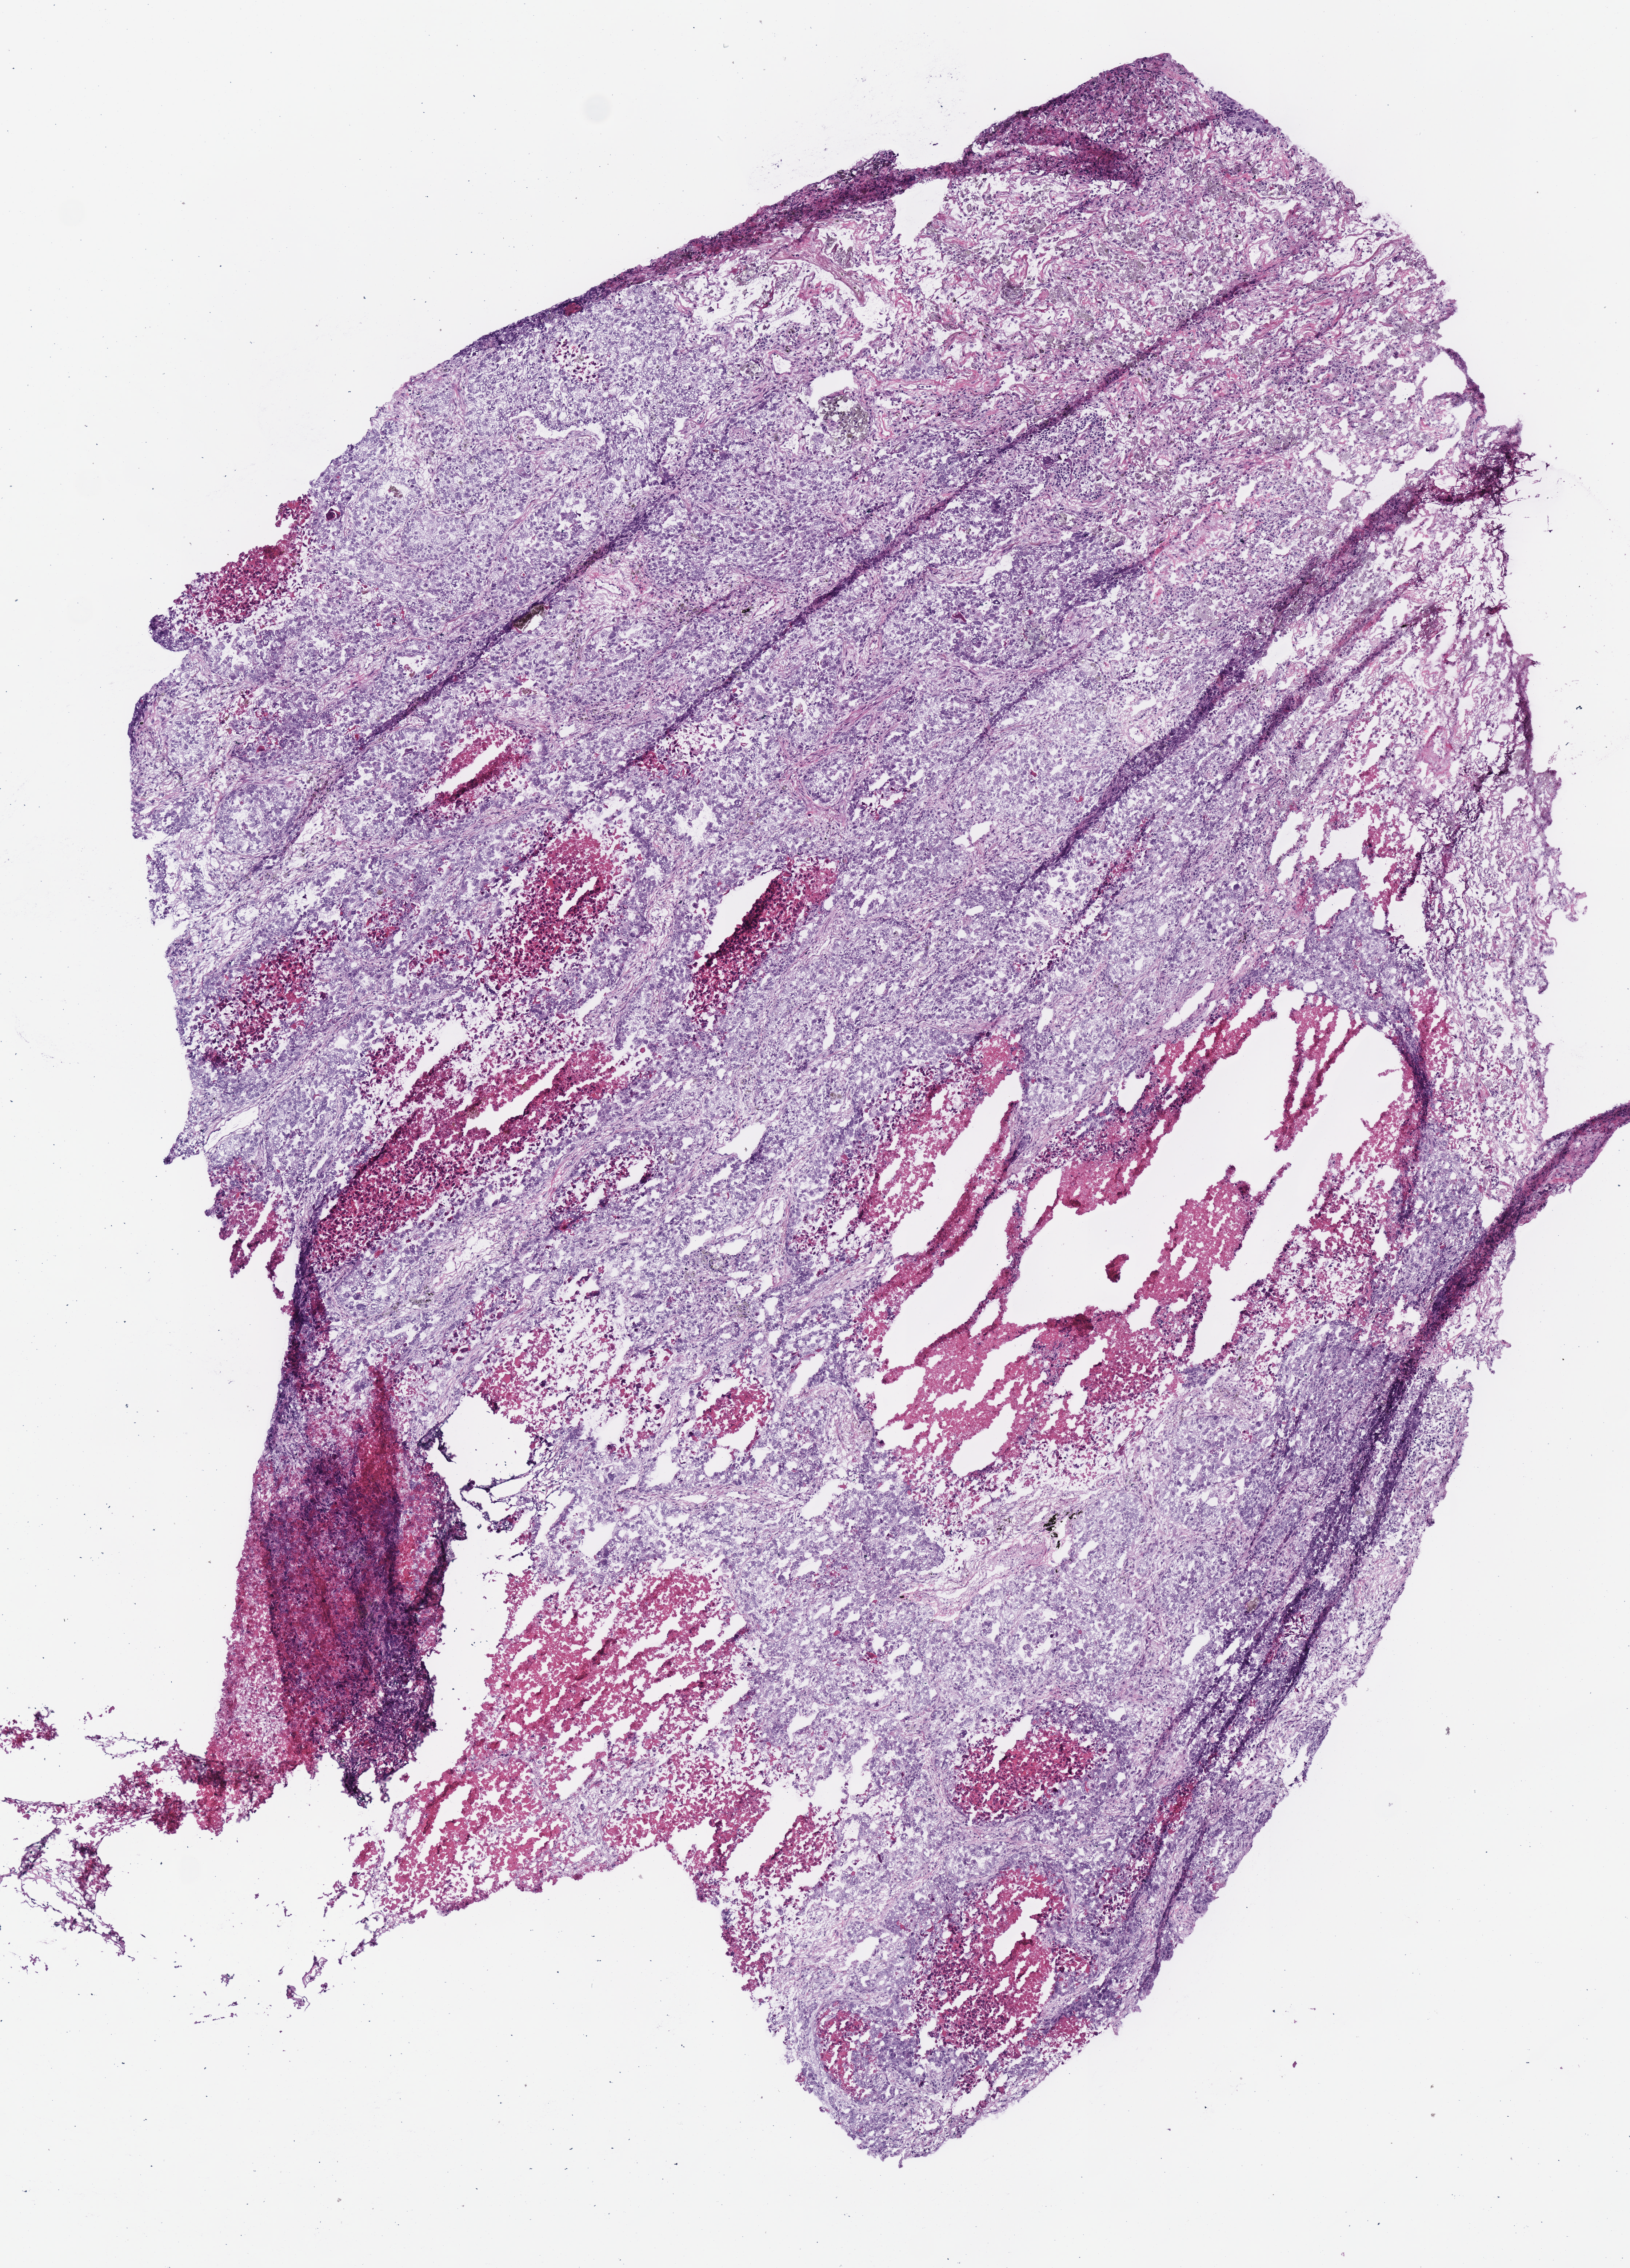
Whole-slide histology image, H&E, low-resolution overview of the scanned area, about 4.4 x 6.1 mm; frozen section; lung, primary tumour sample. Male patient; age at initial diagnosis 62 years. Pathologist review of this section (percent, as recorded): tumour cells 65%, tumour nuclei 70%, normal cells 0%, stromal cells 17%, necrosis 18%. Infiltration values recorded for this section: lymphocyte infiltration 7%.
Histologic diagnosis: Adenocarcinoma with mixed subtypes (upper lobe, lung). AJCC pathologic stage: IIIA (6th edition).